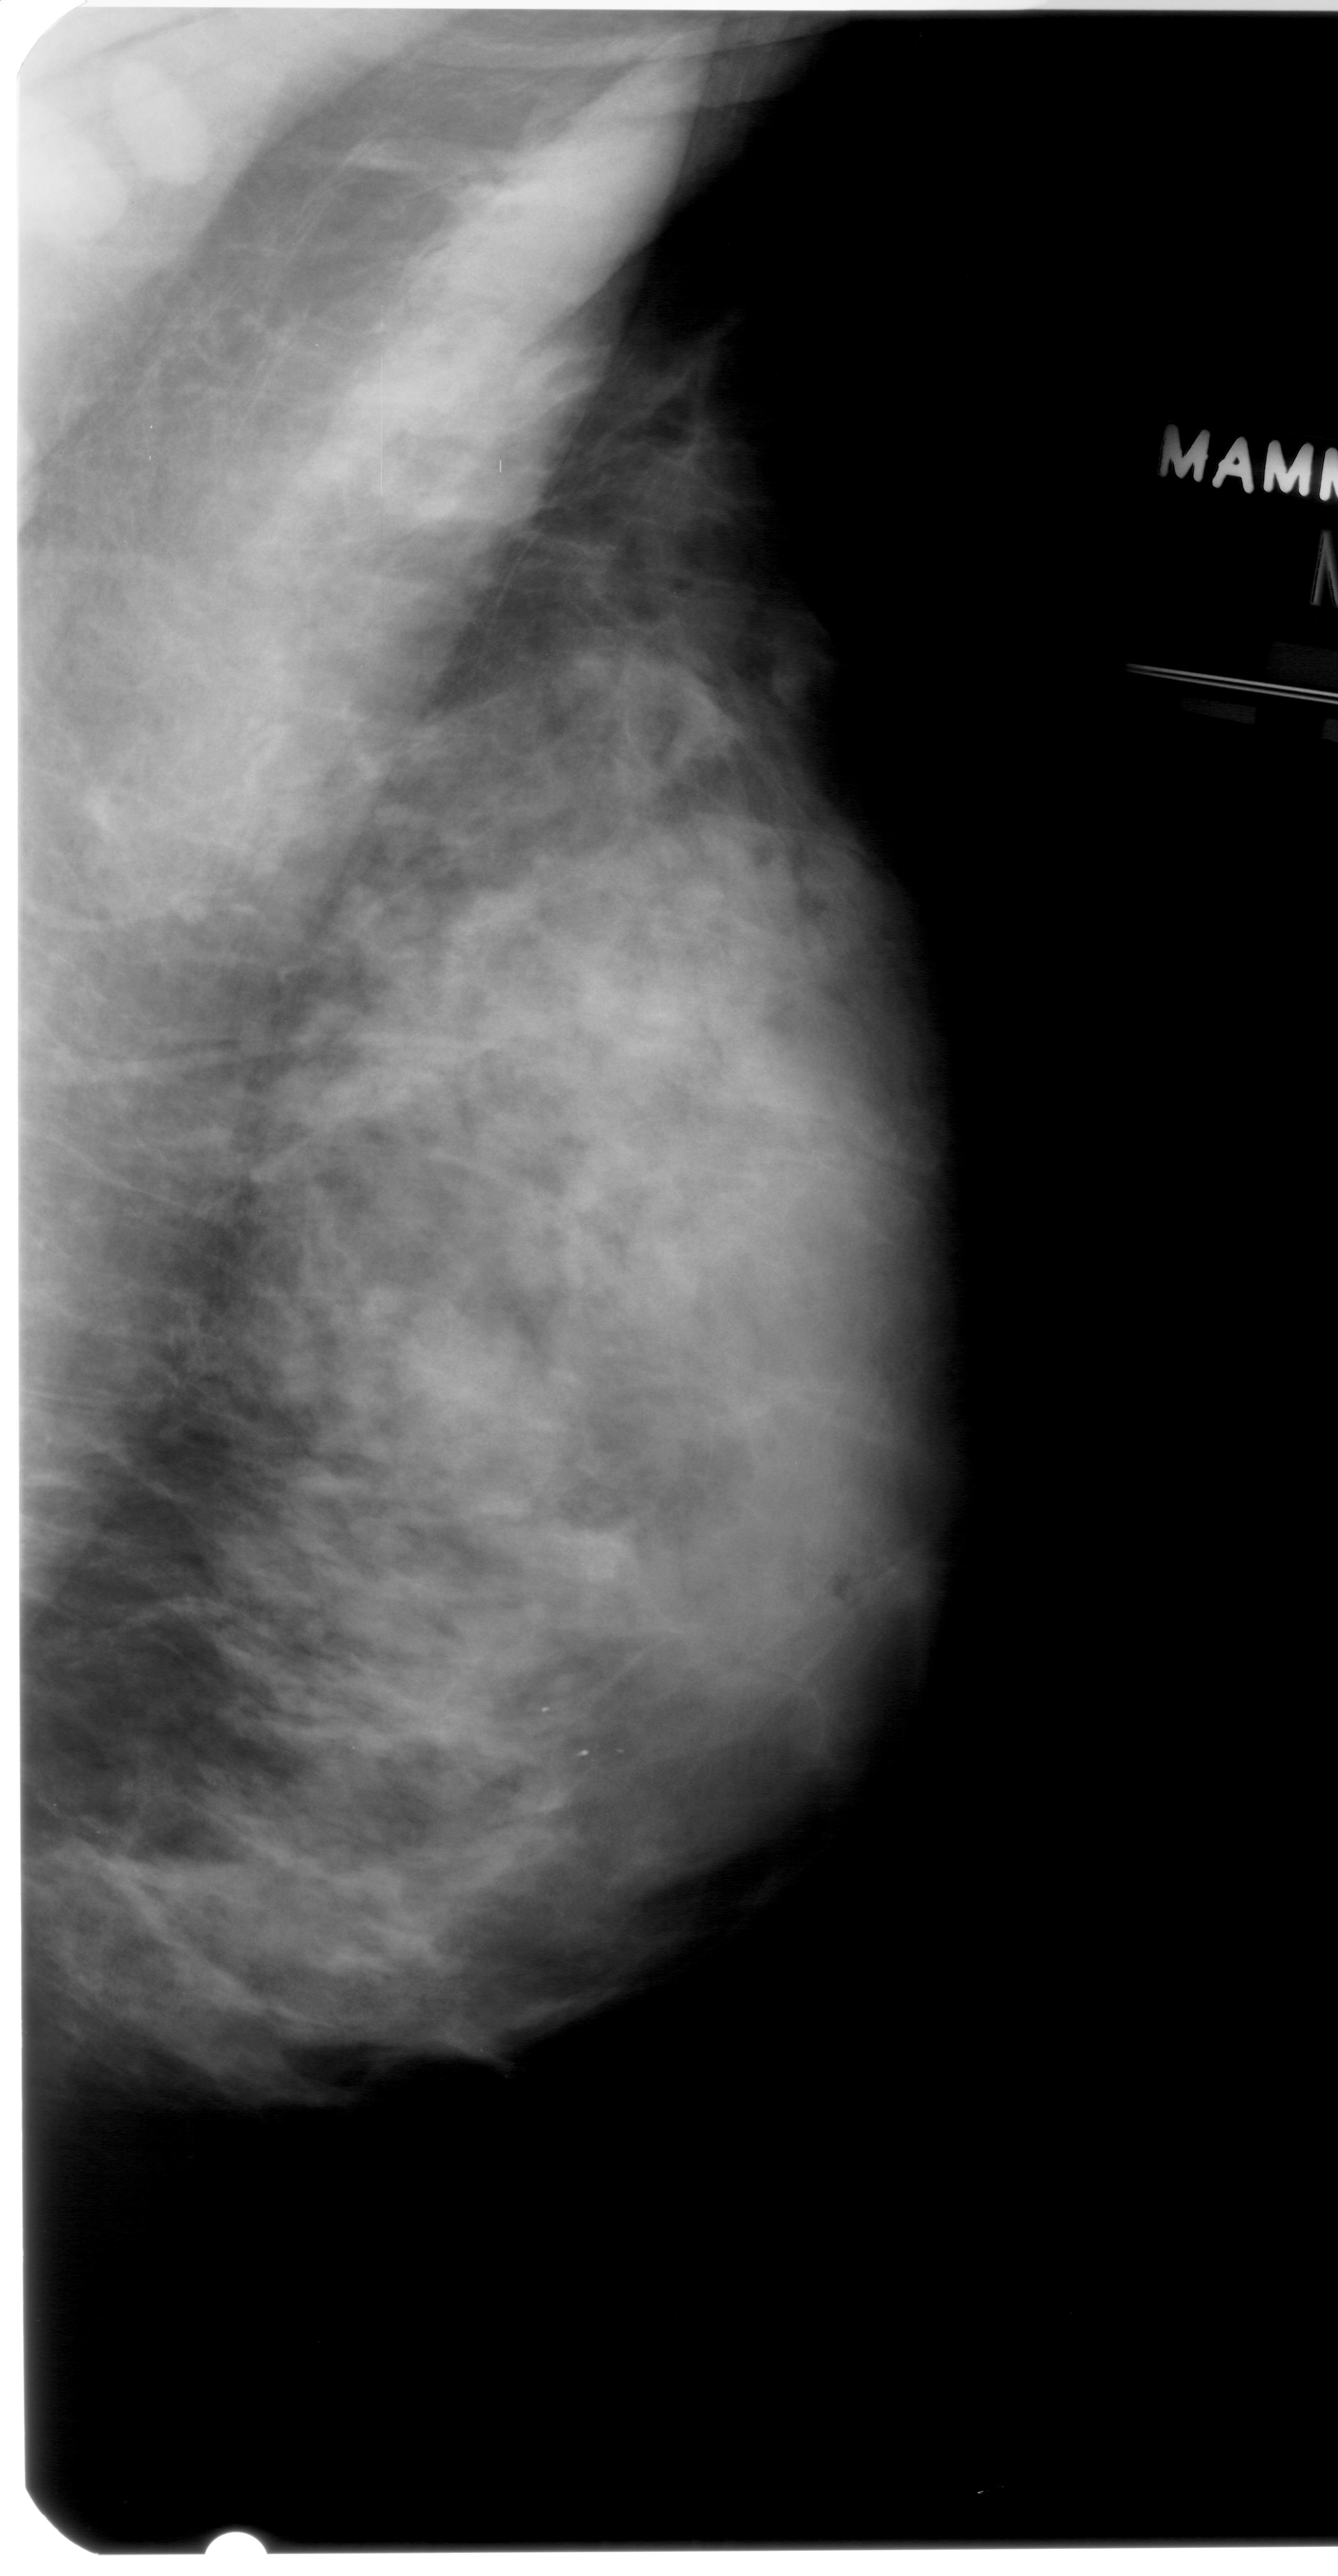
Digitized screen-film mammogram; right breast; mediolateral oblique (MLO) view; BI-RADS breast density category 4 (scale 1–4).
Marked abnormality: calcifications, morphology pleomorphic, distribution clustered; BI-RADS assessment category 4; subtlety rating 4 on a 1 (subtle) to 5 (obvious) scale; pathology result (as recorded, not read from the image): benign.